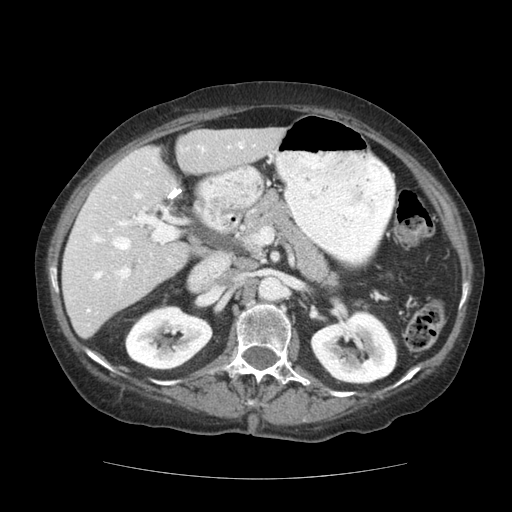
Contrast-enhanced abdominal CT (liver protocol), one axial slice. Reconstruction kernel STANDARD. Soft-tissue window (W 400 / L 40 HU). 512 × 512 image matrix, field of view 360 × 360 mm. From the clinical record (not read from this slice): diagnosis: hepatocellular carcinoma (patient treated with transarterial chemoembolisation; whether this scan precedes or follows treatment is not stated here); TNM stage (as recorded): Stage-I; Child-Pugh class: A; tumour differentiation: moderately-poorly differentiated; tumour nodularity: uninodular.
Annotated regions visible in this slice (semi-automatic segmentation, software-assisted and operator-edited):
- liver parenchyma outside the tumour (the mass and vessels are separate outlines, so this box may not span the whole liver): bounding box [x1, y1, x2, y2] px = [62, 128, 284, 338]
- liver vessels: [74, 141, 255, 313]